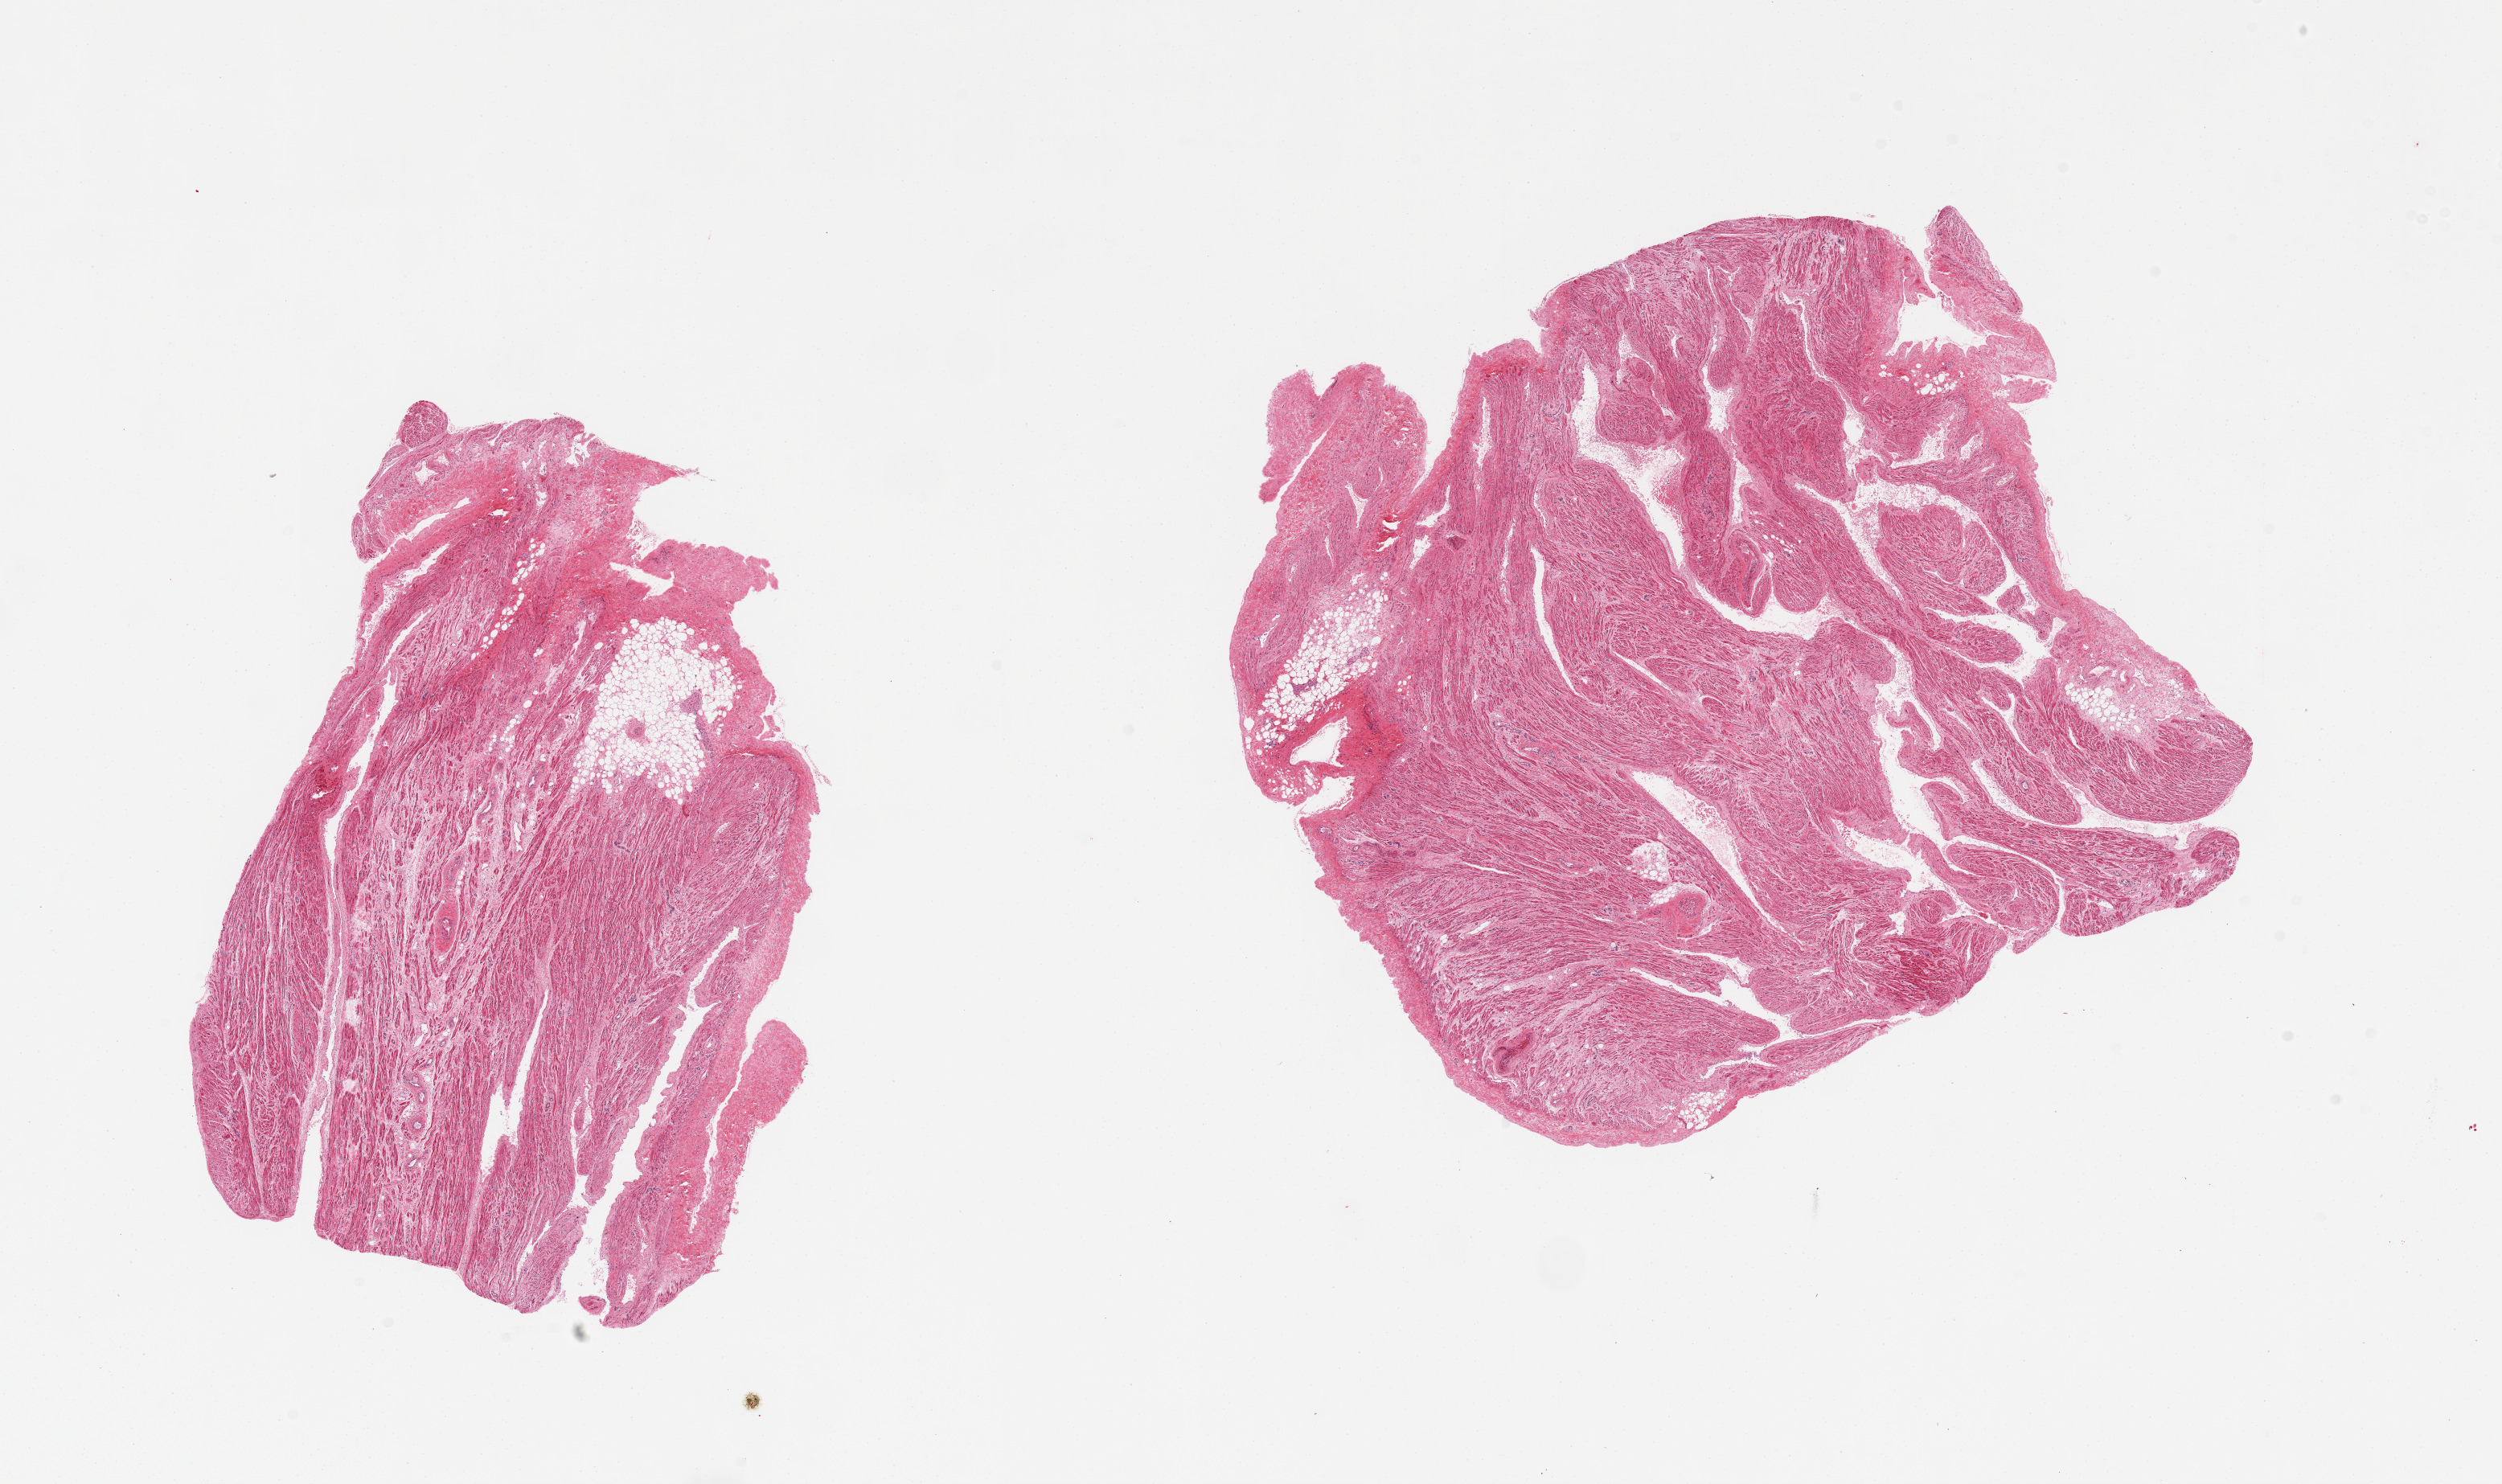
H&E whole-slide image, whole scanned area (about 24.6 x 14.6 mm) shown as a low-resolution overview. PAXgene-fixed, paraffin-embedded tissue. Sampled site (target tissue): auricular appendage. Tissue donor sample. Donor: male.
- review note (as recorded): 2 pieces: 1 with 10% internal fat, 1 with 5% internal fat